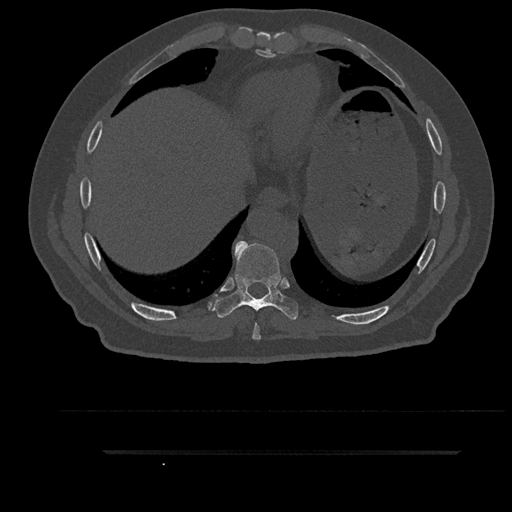
CT including the spine, one axial slice. Position 433 of 797 along the scan axis. Reconstruction kernel Br40s/3. Bone window (W 1800 / L 400 HU). 512 × 512 image matrix. Male patient, age 63 years. Case-level facts recorded for this patient, not image findings: primary cancer: renal.
Structures marked on this image (semi-automatically segmented with operator editing):
- T8 vertebra: bounding box [x1, y1, x2, y2] px = [252, 324, 261, 340]
- T9 vertebra: [212, 241, 298, 320]